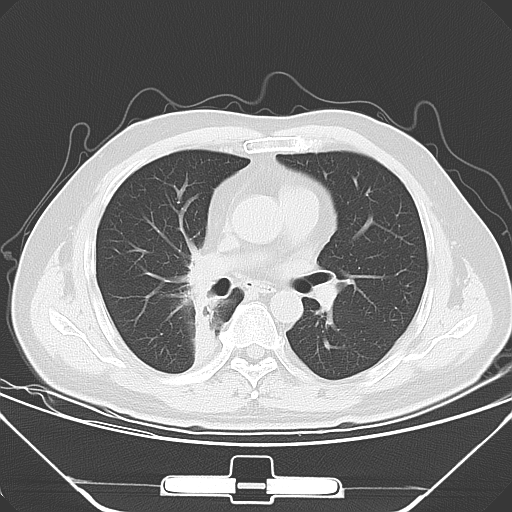
Chest CT, one axial slice; slice 30 of 56 in the series (ordered by position); lung window (W 1500 / L -600 HU); 5 mm slice thickness; 512 × 512 image matrix, field of view 371 × 371 mm. Patient: male, 48 years. Case-level facts recorded for this patient, not image findings: clinical TNM (as recorded): T1a N1 M1c.
Annotated regions visible in this slice (bounding box drawn by a radiologist):
- lung tumour (recorded histology: adenocarcinoma): box from (x=178, y=243) to (x=215, y=361) px